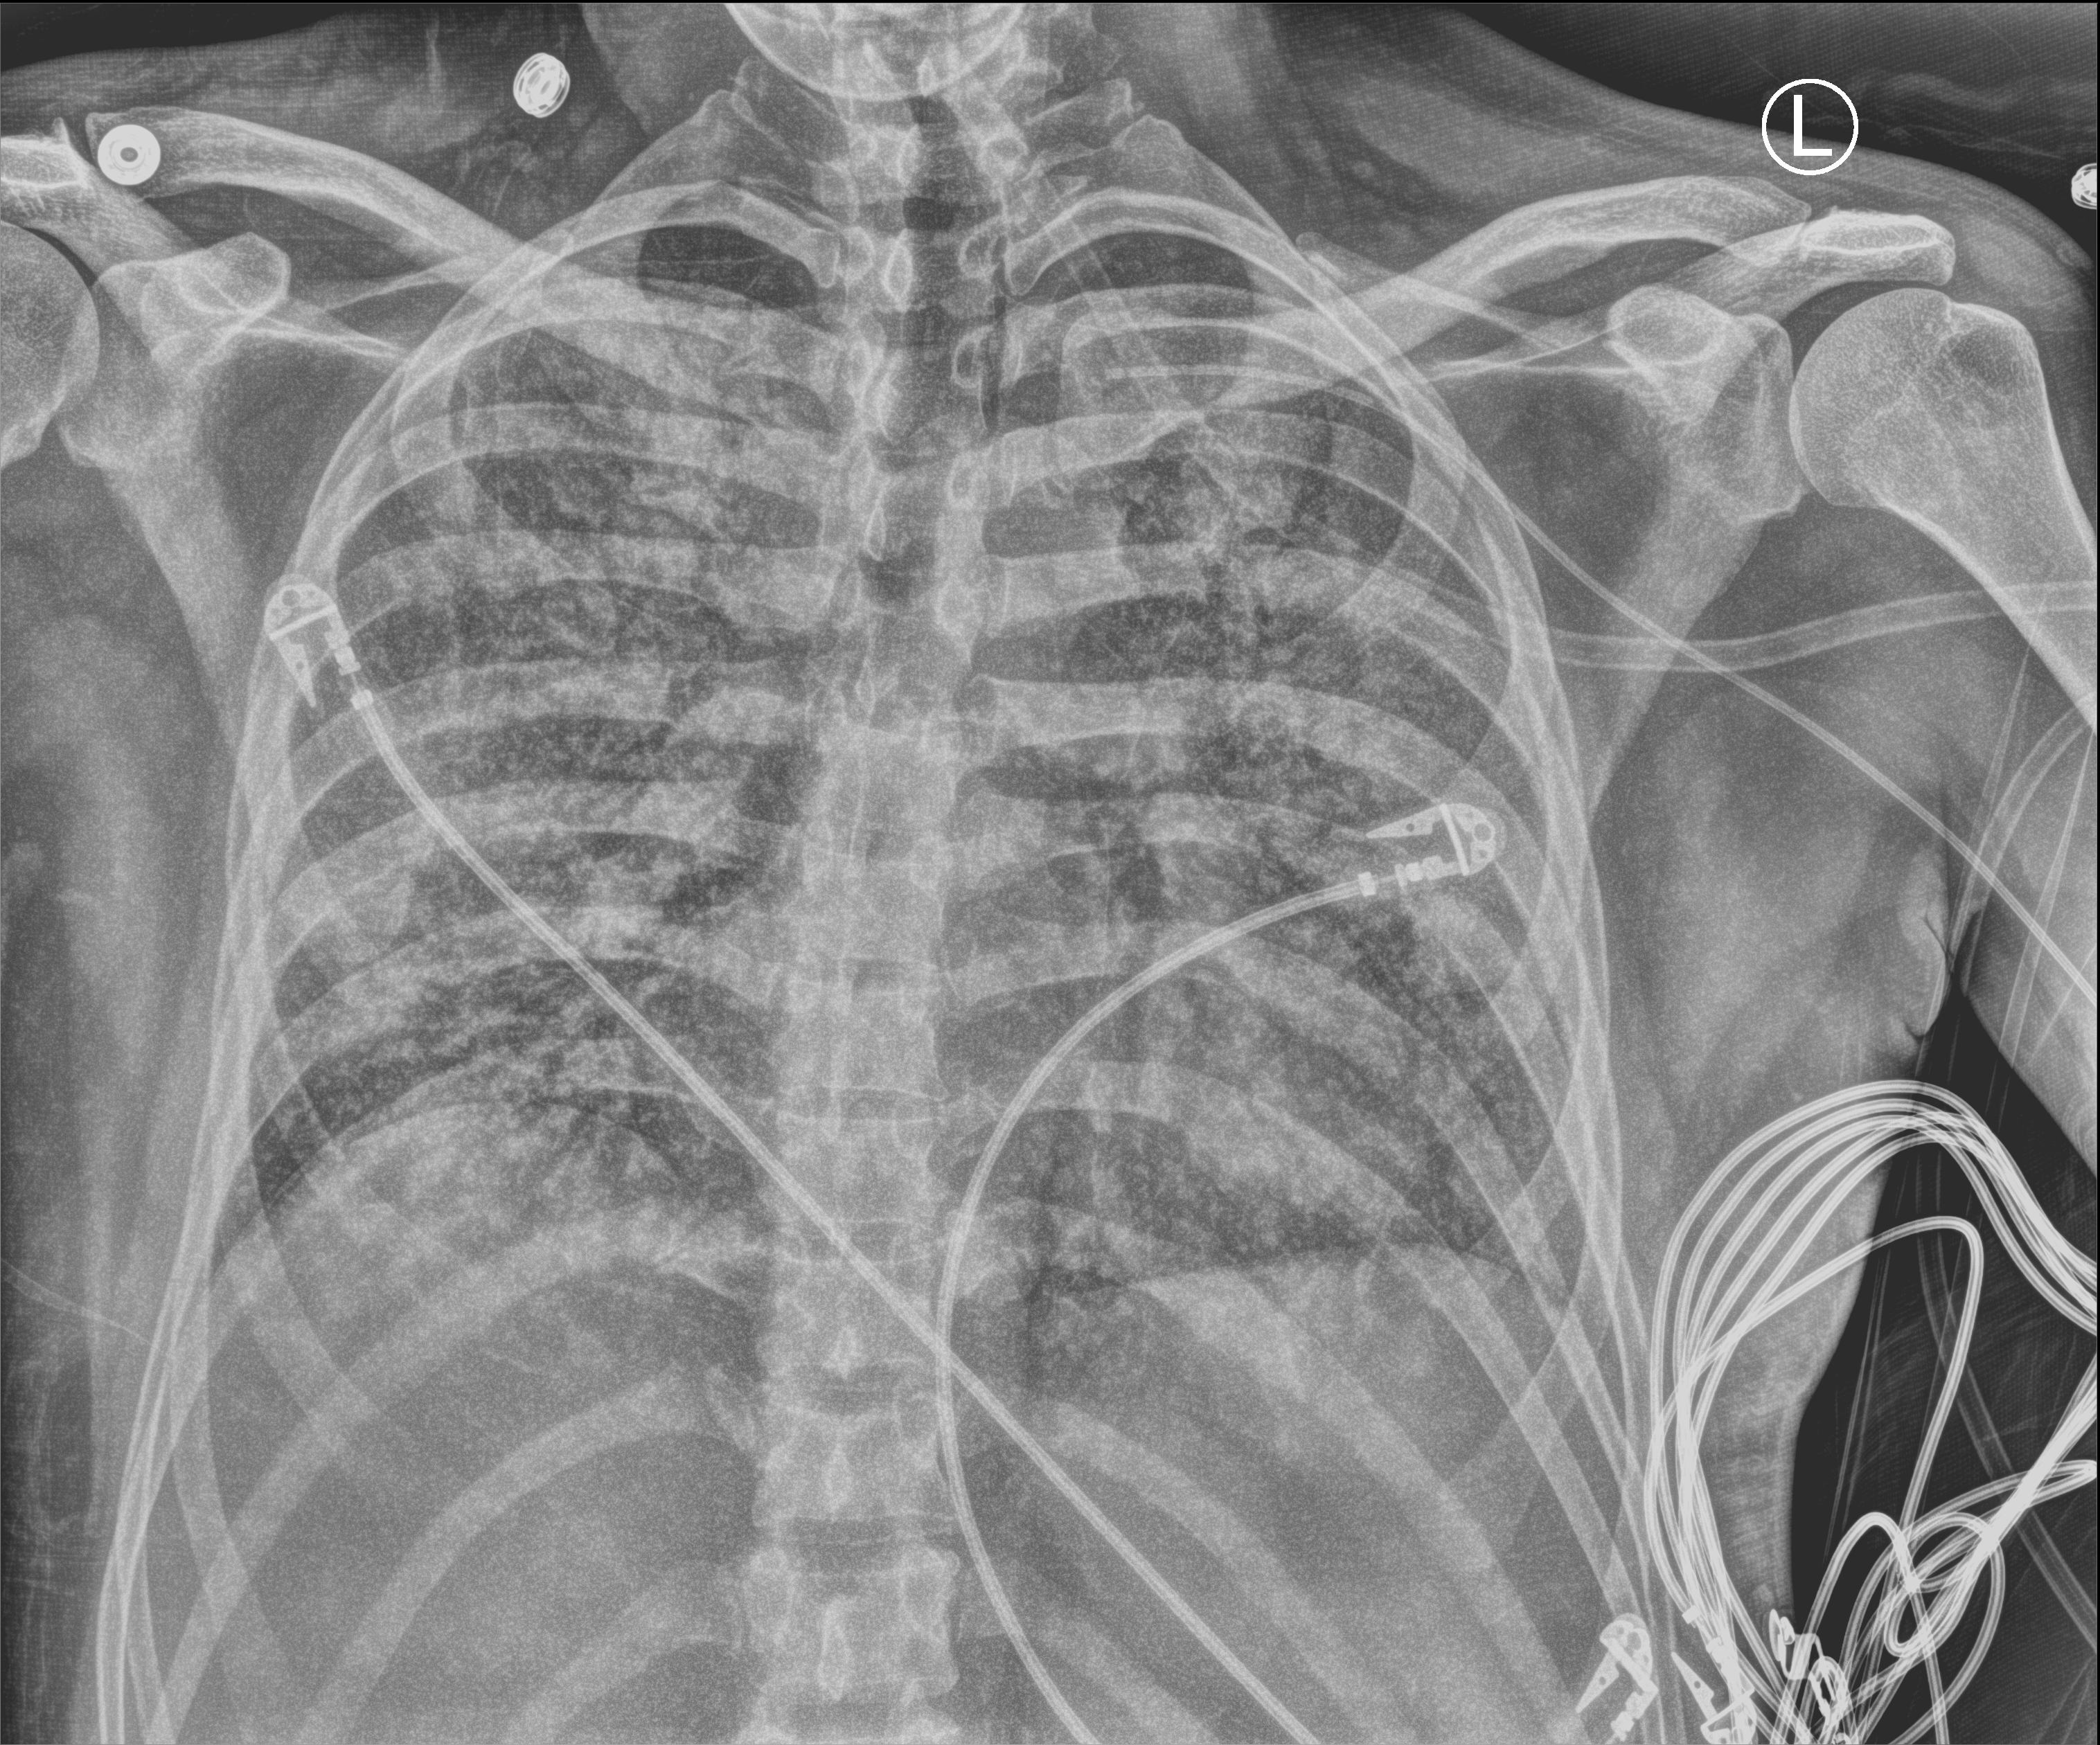
Chest X-ray (portable), anteroposterior (AP) projection. Patient hospitalised with COVID-19; male, aged 18–59 years.
Admission-level facts for this patient (not findings on this image; timing relative to this image not recorded):
- other chronic lung disease (admission record): no
- admitted to intensive care during this hospital stay: yes
- mechanically ventilated during this hospital stay: yes